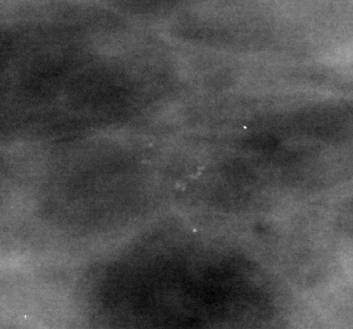
Region of interest cut from a scanned film mammogram (one marked finding), right breast, MLO view, BI-RADS breast density category 3 (scale 1–4).
Finding: calcifications, morphology pleomorphic, distribution clustered; BI-RADS assessment category 4; subtlety rating 3 on a 1 (subtle) to 5 (obvious) scale; pathology (as recorded): benign.